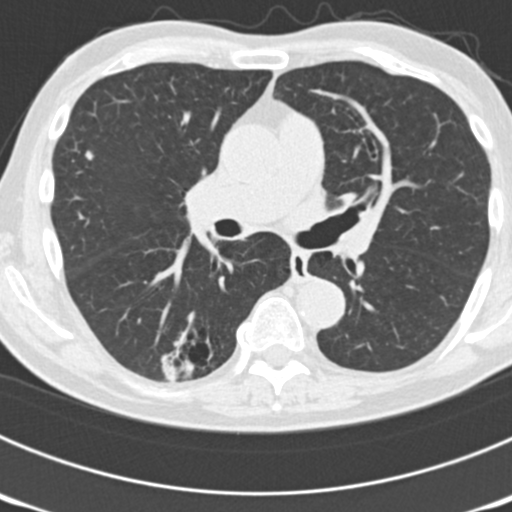
Low-dose screening chest CT, one axial slice; position 106 of 177 along the scan axis; reconstruction kernel B30f; 120 kVp; lung window (W 1500 / L -600 HU); 2 mm slice thickness; 512 × 512 image matrix, field of view 300 × 300 mm.
Structures marked on this image (expert manual segmentation):
- lesion 2 (nodule, upper lobe of right lung): bounding box (x1, y1, x2, y2) in pixels: (85, 150, 95, 161)
- lesion 5 (nodule, lower lobe of right lung): (163, 353, 195, 379)